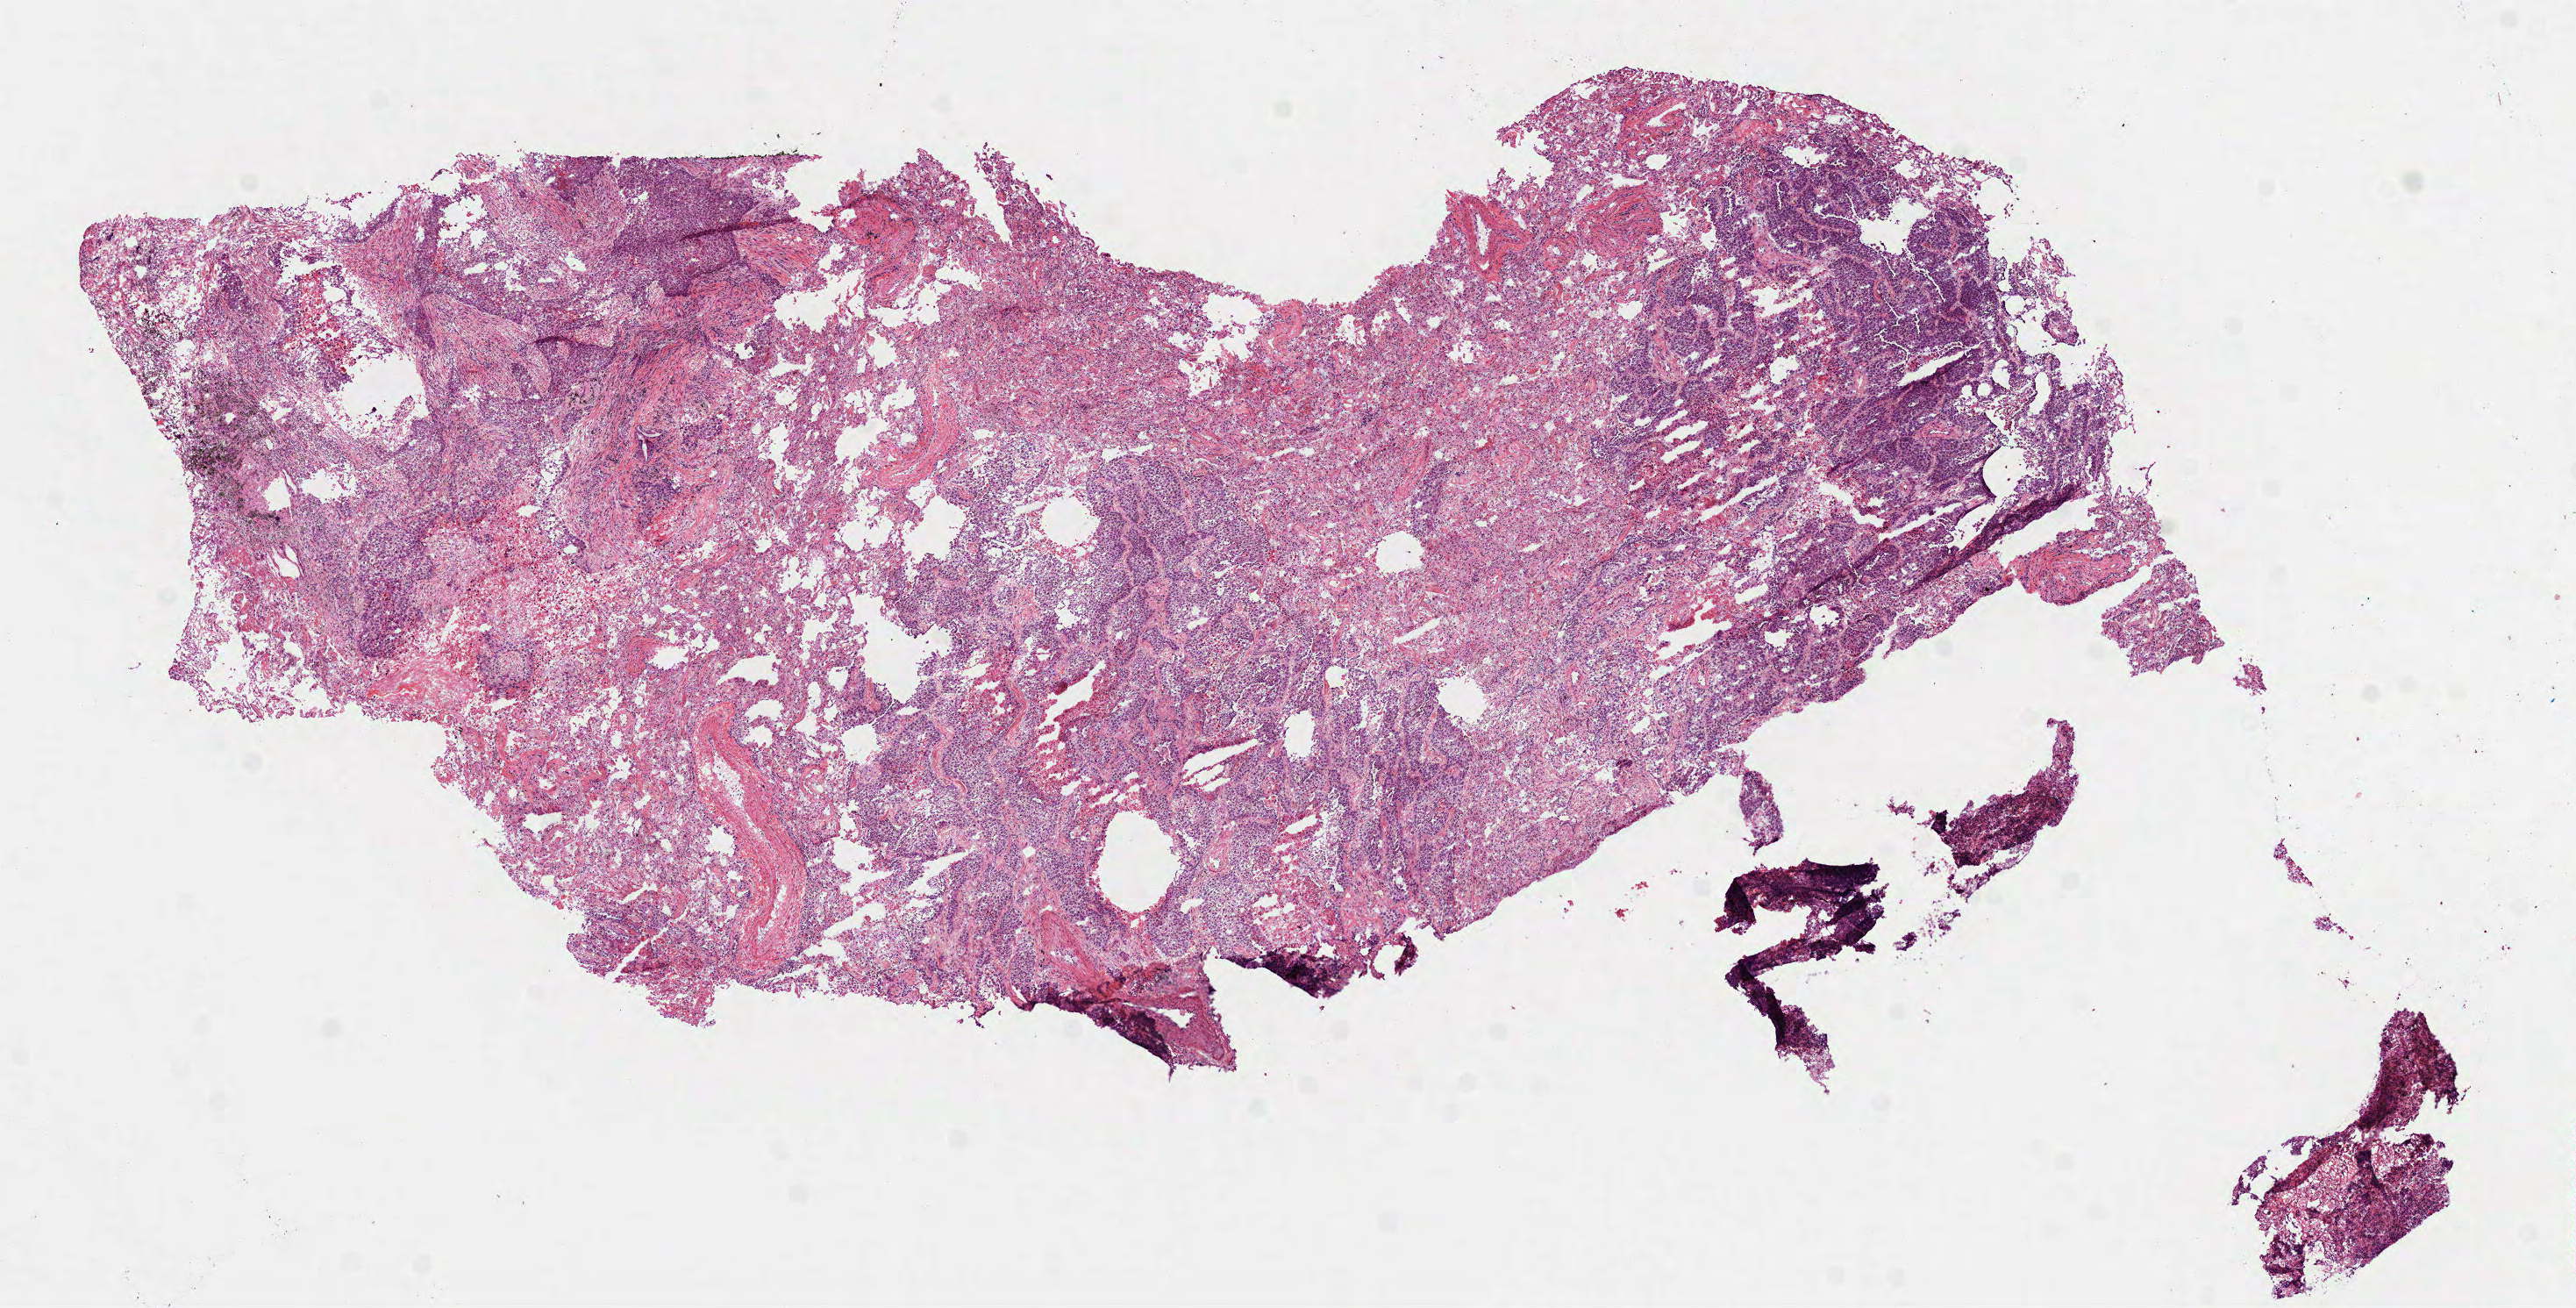
Digitized H&E tissue section (whole slide) — shown as a low-resolution overview of the whole scanned area (about 11.8 x 6.0 mm, slide scanned at 40x). Frozen section. Sample: primary tumour, lung. Patient: female, age at initial diagnosis 59 years. Slide review estimates, as recorded: tumour cells 80%, tumour nuclei 65%, normal cells 0%, stromal cells 20%, necrosis 0%.
AJCC pathologic stage: IB. Diagnosis: Squamous cell carcinoma, NOS (upper lobe, lung). Laterality: left. TNM: T2 N0 M0.